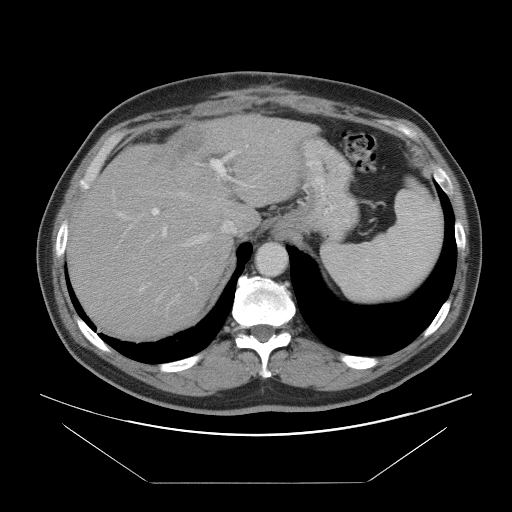
Contrast-enhanced abdominal CT, one axial slice. Intravenous contrast given. Soft-tissue window (W 400 / L 40 HU). 512 × 512 image matrix, field of view 442 × 442 mm. Male patient, age 62 years. Case-level facts recorded for this patient, not image findings: diagnosis: colorectal cancer liver metastases, imaged before liver resection; multiple liver metastases: no; largest metastasis: 7 cm; disease in both lobes: yes.
Structures marked on this image (expert manual segmentation):
- hepatic veins: bounding box [x1, y1, x2, y2] px = [152, 139, 286, 256]
- liver: [70, 114, 305, 338]
- planned liver remnant (the part of the liver to remain after resection): [70, 170, 231, 337]
- portal vein (with intrahepatic branches): [118, 146, 252, 292]
- liver metastasis: [148, 125, 207, 171]